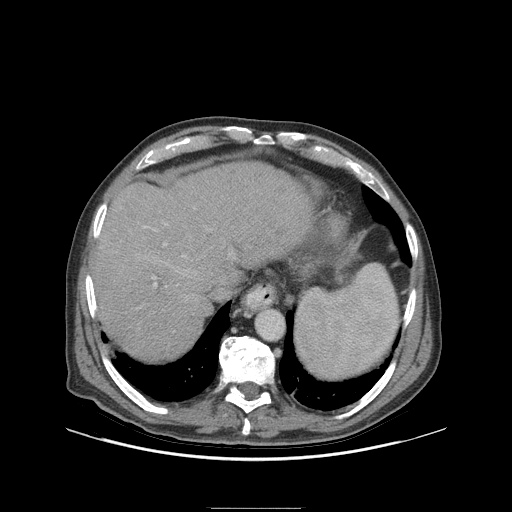
Contrast-enhanced abdominal CT (liver protocol), one axial slice; position 80 of 105 along the scan axis; reconstruction kernel STANDARD; soft-tissue window (W 400 / L 40 HU); 2.5 mm slice thickness; 512 × 512 image matrix, field of view 440 × 440 mm. From the clinical record (not read from this slice): diagnosis: hepatocellular carcinoma (patient treated with transarterial chemoembolisation; whether this scan precedes or follows treatment is not stated here); TNM stage (as recorded): Stage-I; Child-Pugh class: A; tumour nodularity: uninodular.
Structures marked on this image (semi-automatic segmentation, software-assisted and operator-edited):
- abdominal aorta: bounding box <256,310,283,339> (left, top, right, bottom; pixels)
- liver parenchyma outside the tumour (the mass and vessels are separate outlines, so this box may not span the whole liver): <92,162,312,358>
- liver vessels: <144,224,185,287>